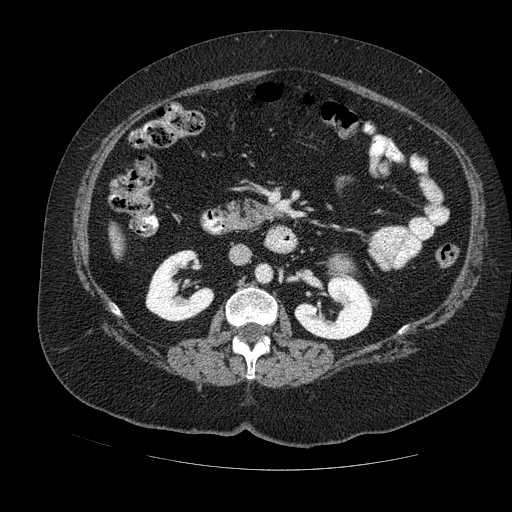
Contrast-enhanced abdominal CT, one axial slice; position 54 of 121 along the scan axis; soft-tissue window (W 400 / L 40 HU); 512 × 512 image matrix, field of view 420 × 420 mm. Female patient. From the clinical record (not read from this slice): diagnosis: adrenocortical carcinoma; tumour side: left adrenal; tumour size at pathology: 8 cm.
Outlined on this slice (semi-automatically segmented with operator editing):
- mass: box from (x=332, y=255) to (x=352, y=271) px